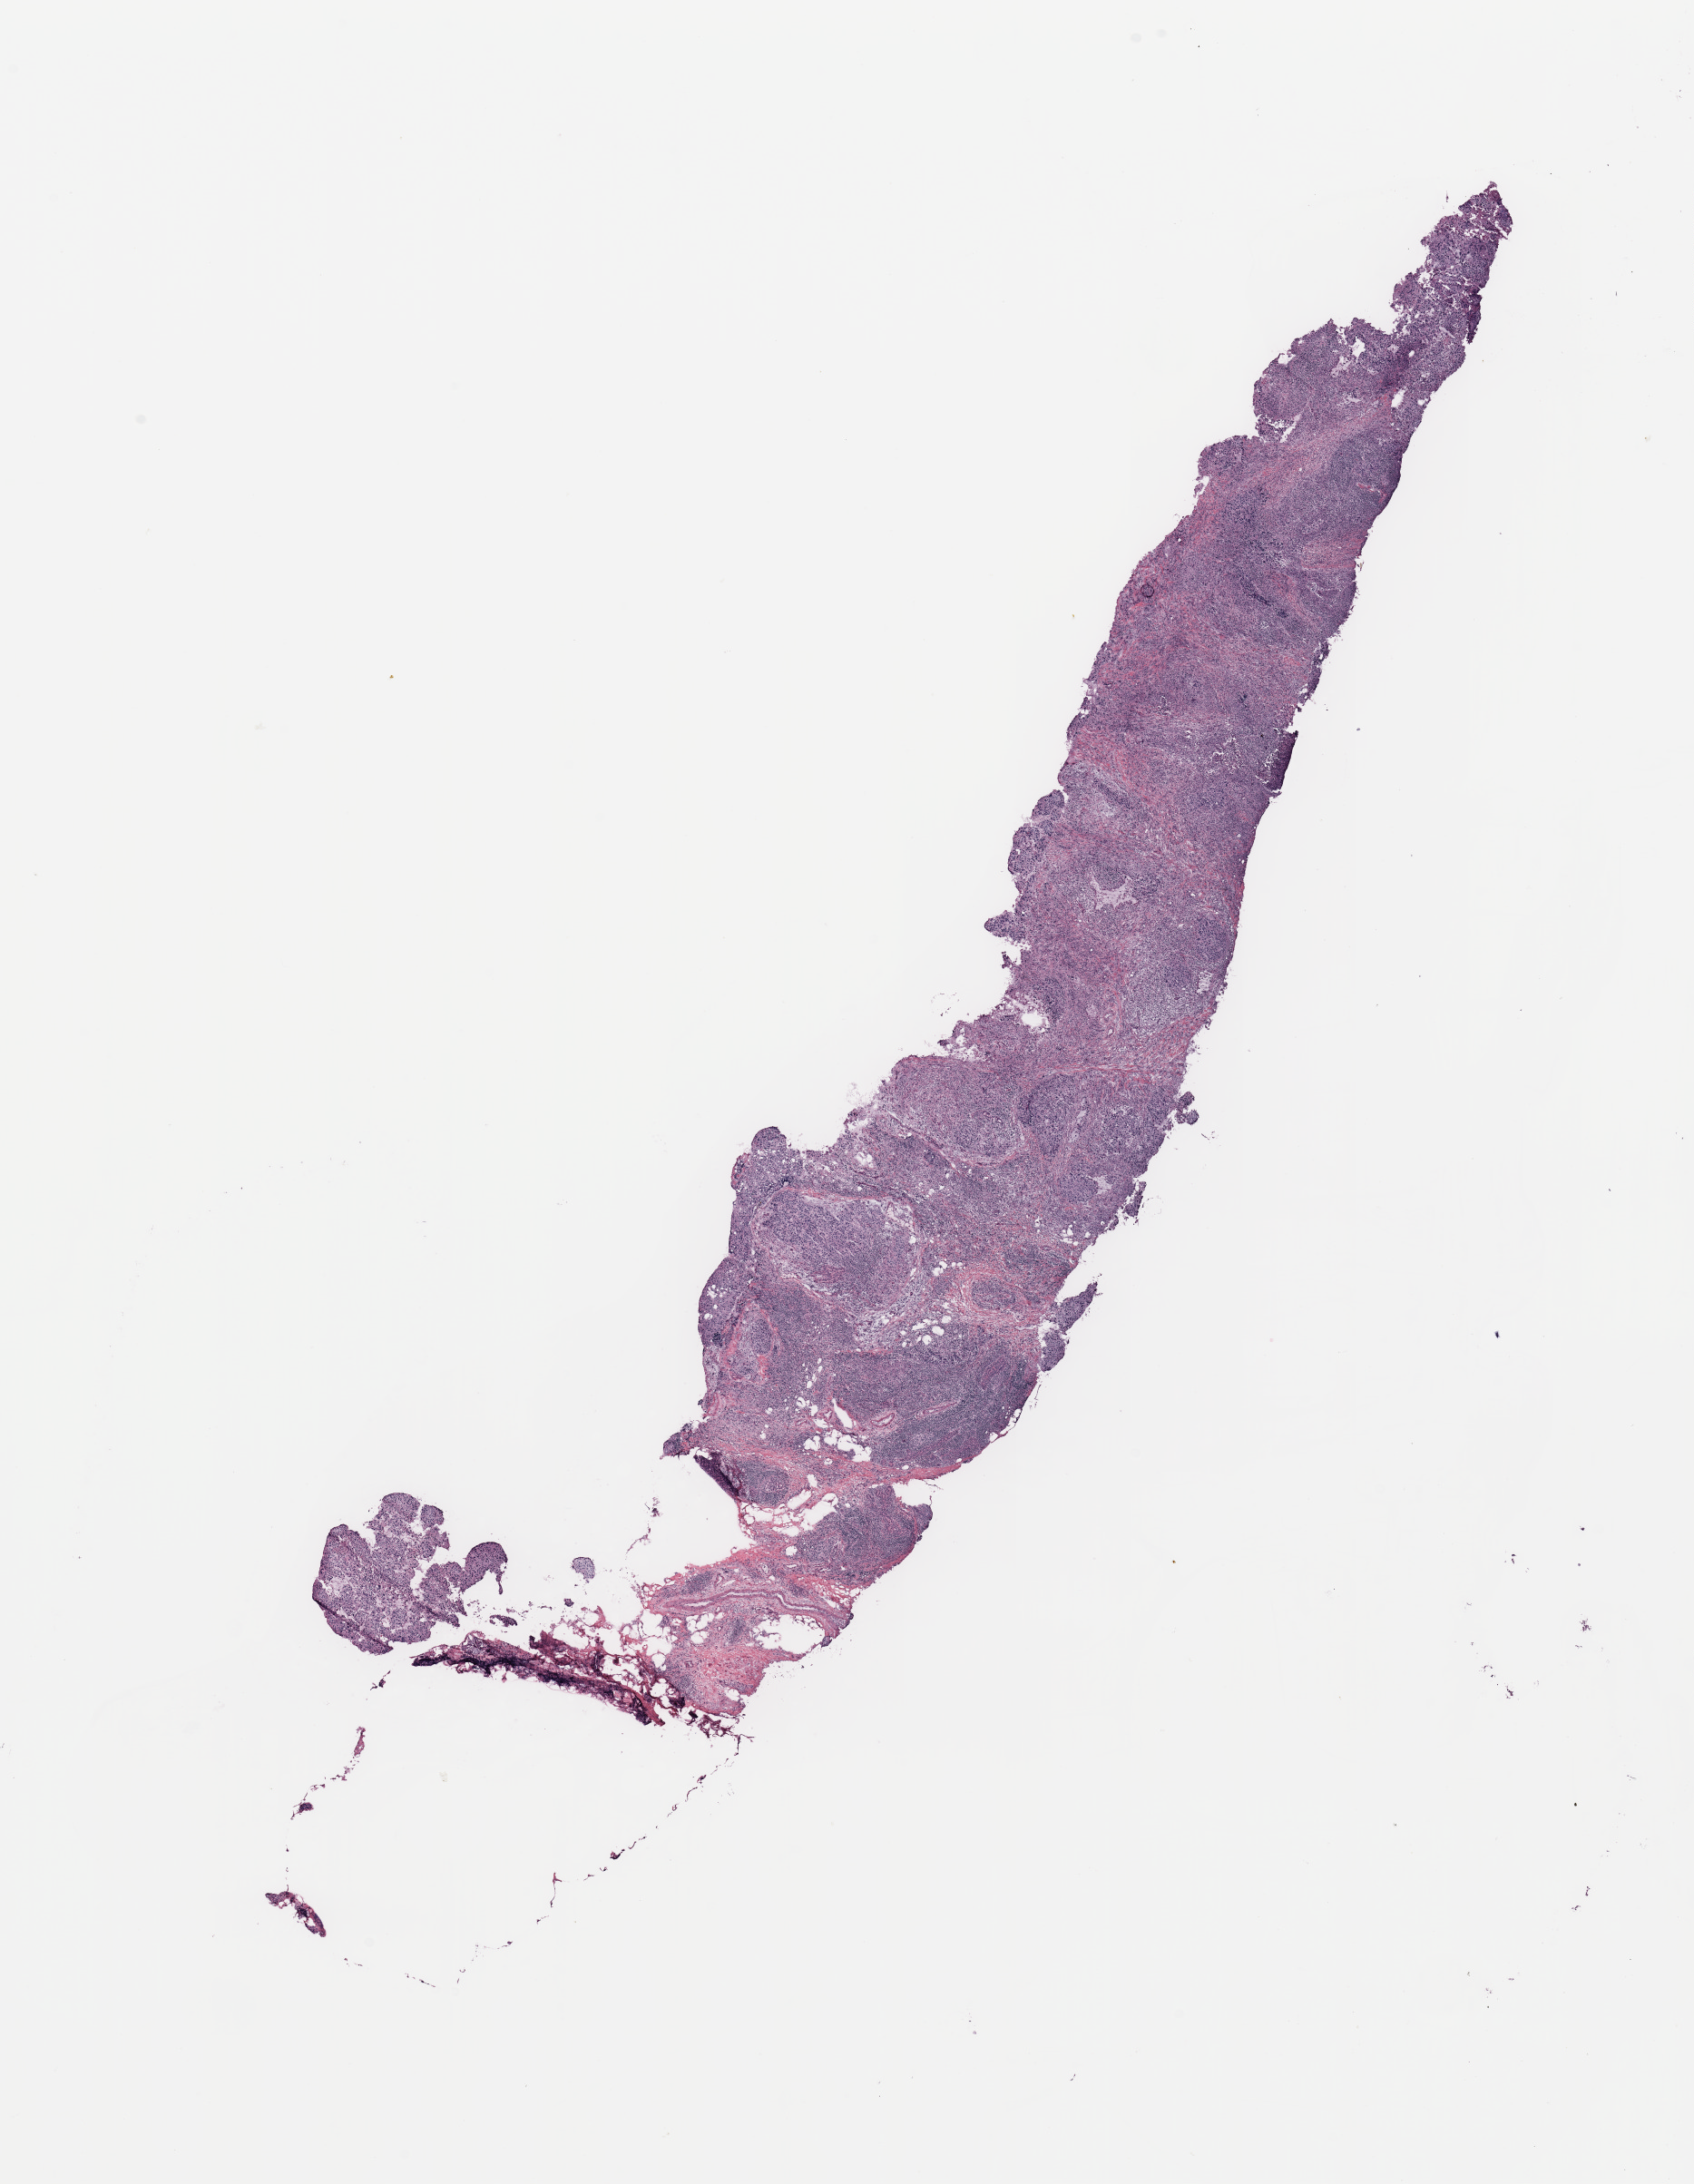
Whole-slide histology image, H&E — shown as a low-resolution overview of the whole scanned area (about 14.8 x 19.0 mm); breast, tissue type not recorded.
Patient diagnosis (cohort enrolment): breast cancer (breast).